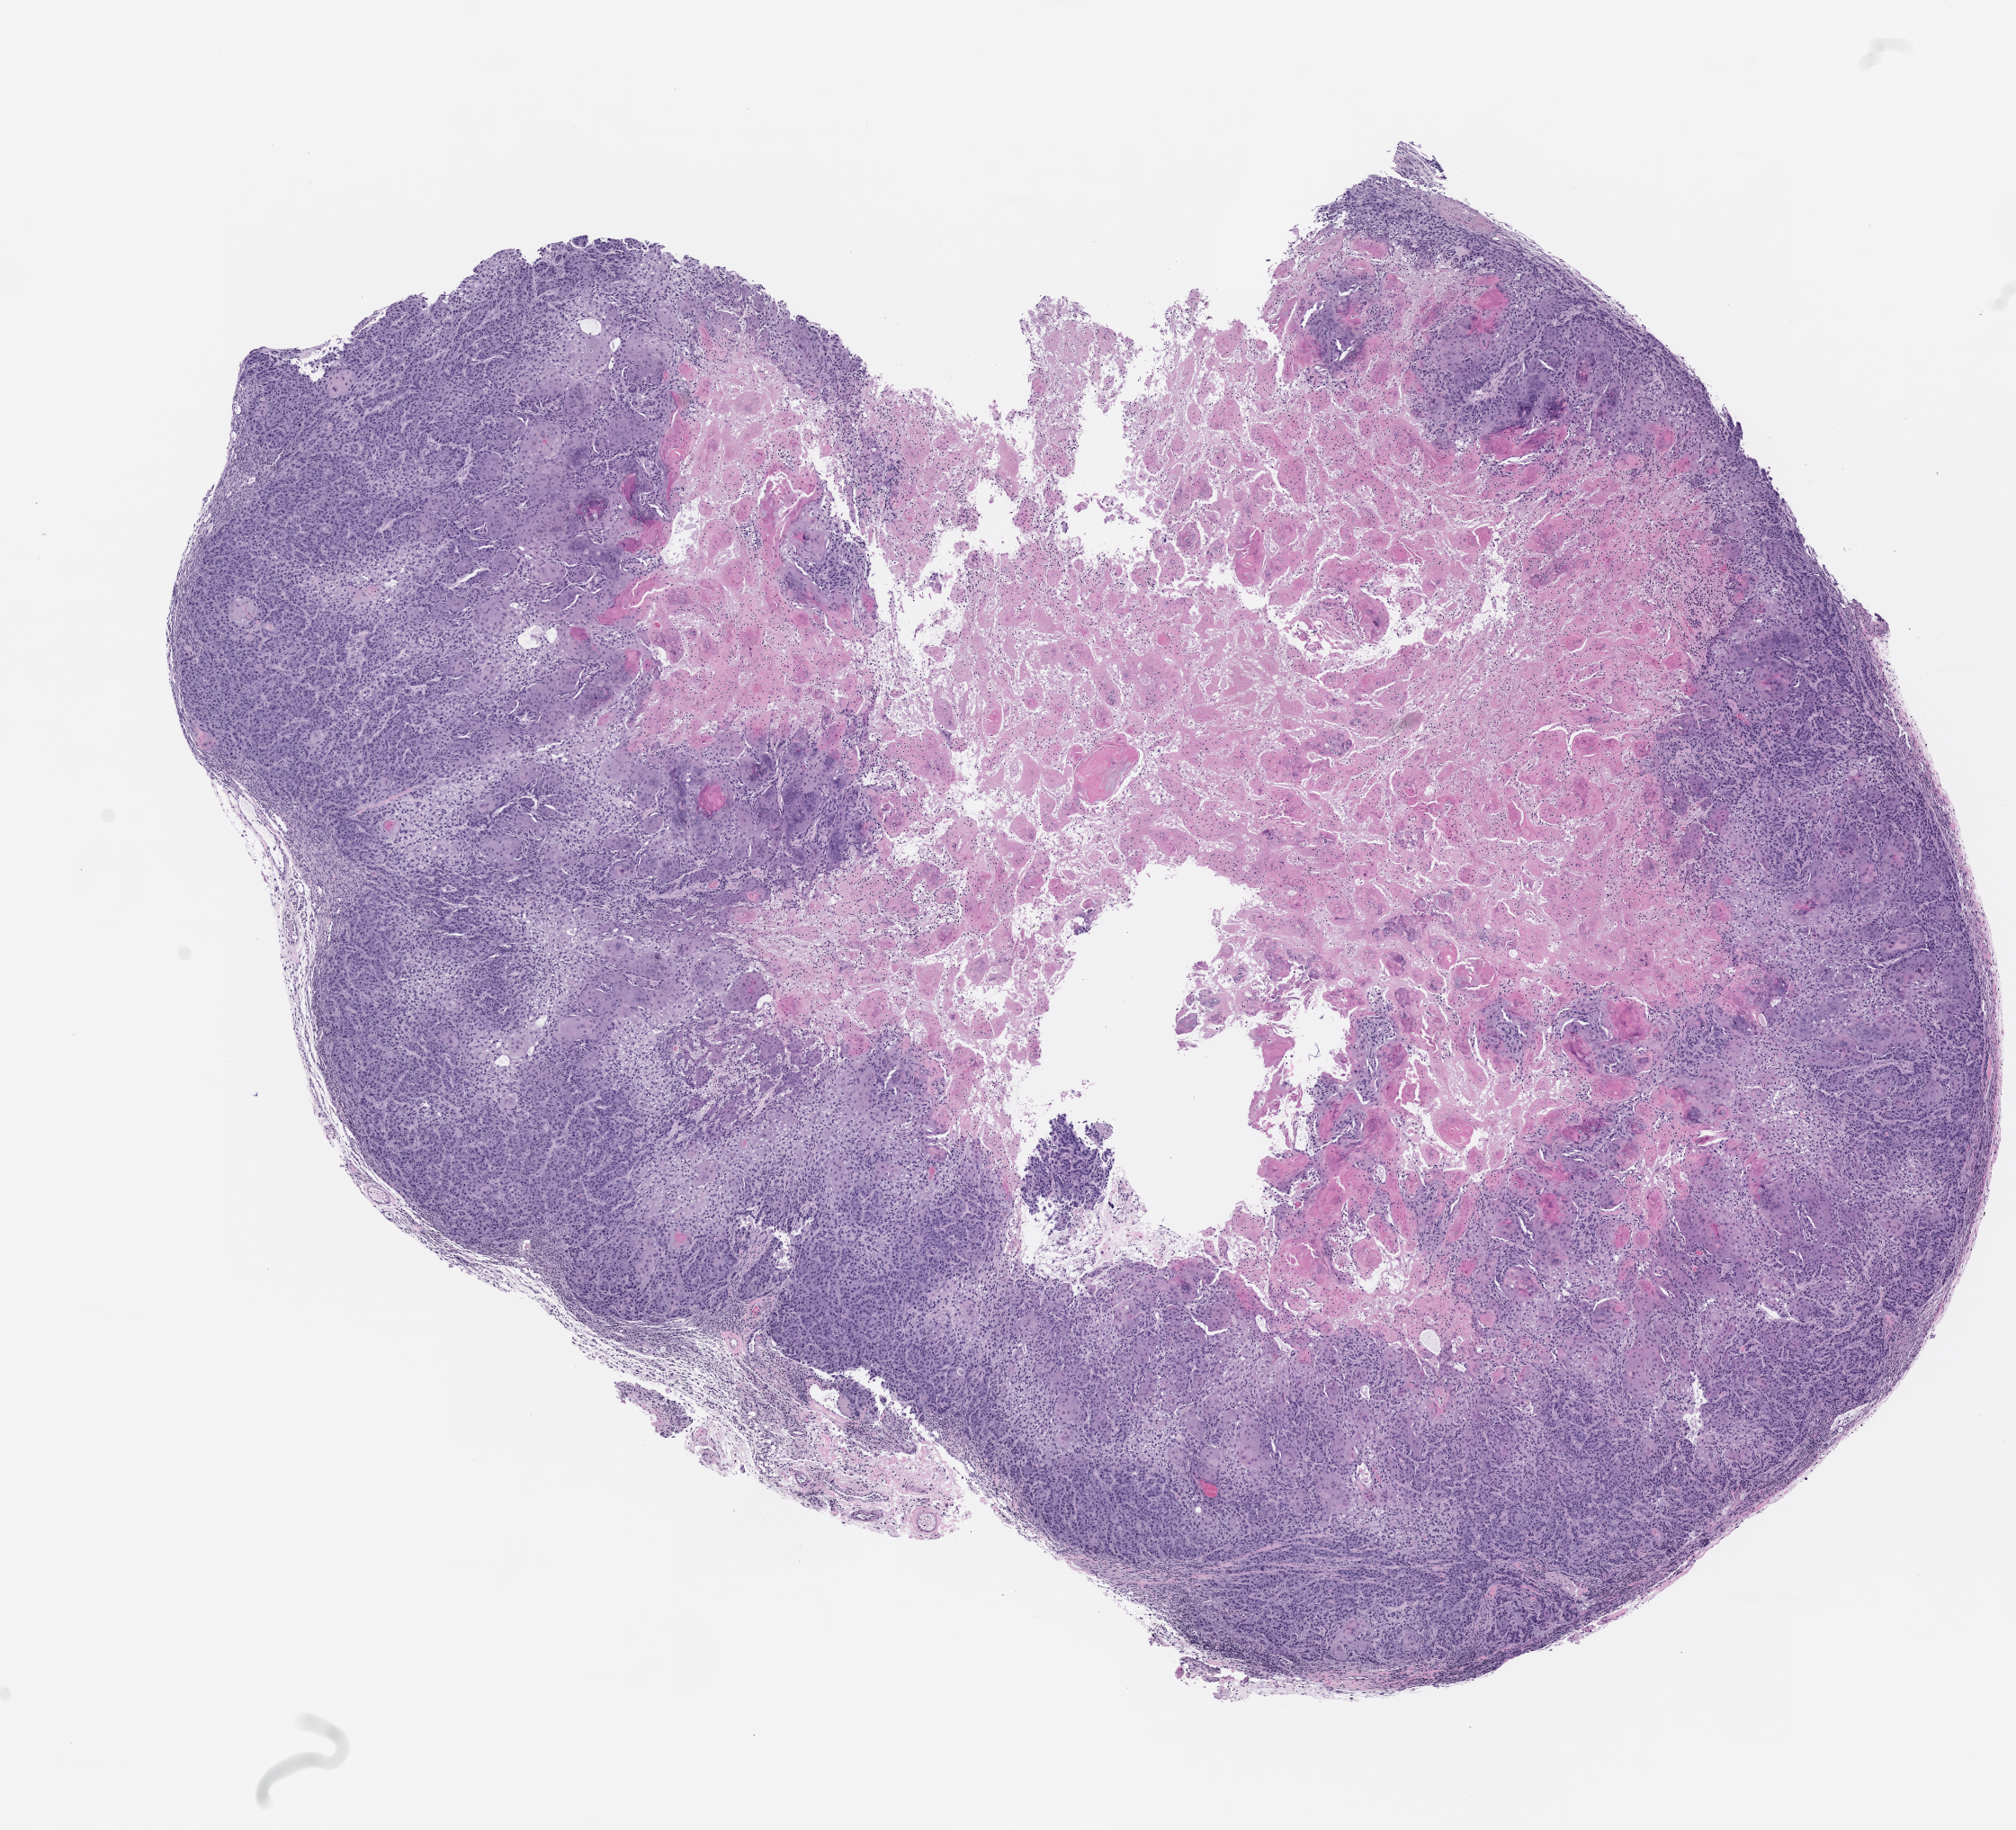
Haematoxylin and eosin whole-slide image of a patient-derived xenograft (PDX) tumor grown in a mouse, passage 3, whole scanned area (about 9.0 x 8.2 mm) shown as a low-resolution overview; formalin-fixed paraffin-embedded section; originating tumor site category: oral soft tissue.
- originating patient diagnosis: Head and Neck Squamous Cell Carcinoma